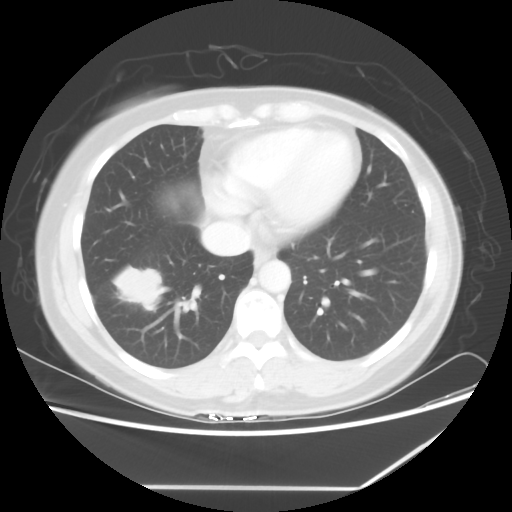
Chest CT, one axial slice. Slice 22 of 60 in the series (ordered by position). Reconstruction kernel STANDARD. Lung window (W 1500 / L -600 HU). 5 mm slice thickness. 512 × 512 image matrix, field of view 374 × 374 mm. Female patient, age 42 years. Case-level facts recorded for this patient, not image findings: clinical TNM (as recorded): T2 N1 M0.
Structures marked on this image (rectangle marked by the reading radiologist):
- lung tumour (recorded histology: adenocarcinoma): bounding box (x1, y1, x2, y2) in pixels: (109, 259, 169, 315)